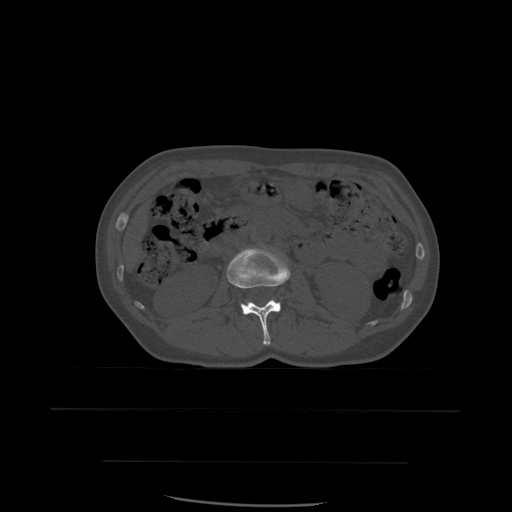
CT including the spine, one axial slice; position 220 of 574 along the scan axis; bone window (W 1800 / L 400 HU); 1.25 mm slice thickness; 512 × 512 image matrix, field of view 392 × 392 mm. Patient age 48 years. From the clinical record (not read from this slice): primary cancer: lung; vertebrae with lytic lesions (as recorded): T11.
Outlined on this slice (semi-automatically segmented with operator editing):
- L2 vertebra: bounding box [x1, y1, x2, y2] px = [227, 248, 291, 346]